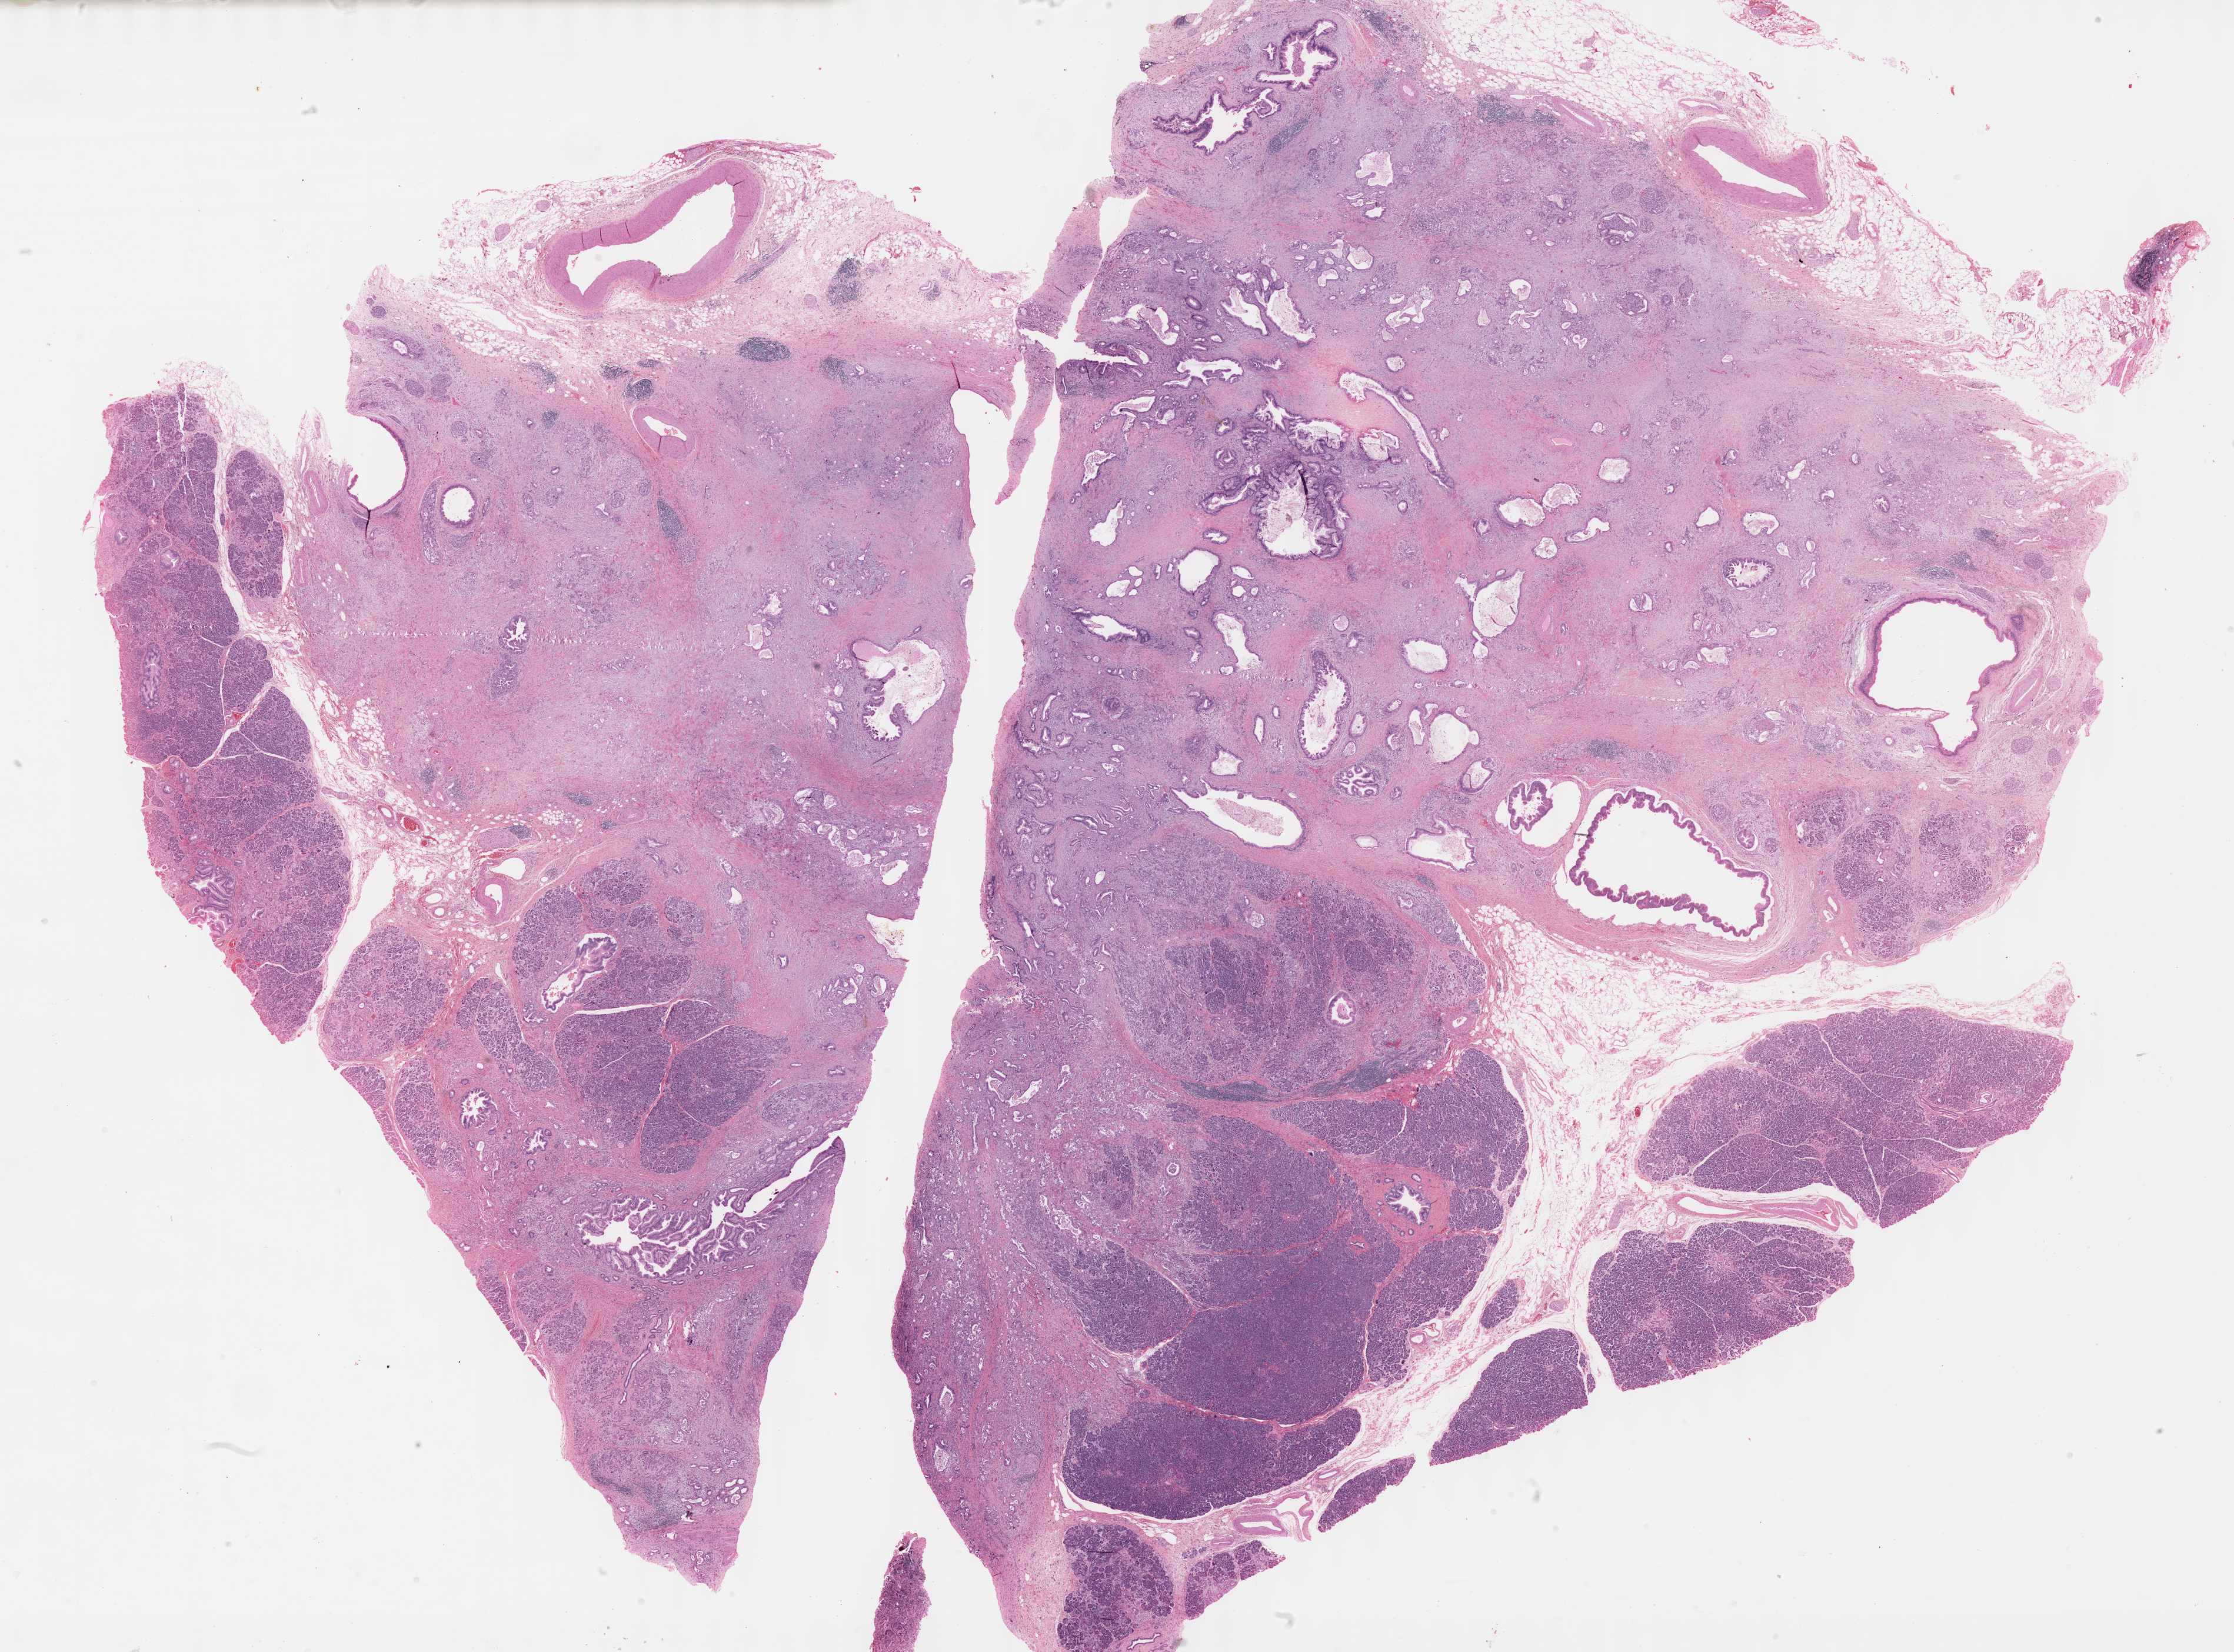
Whole-slide histology image, H&E, shown as a low-resolution overview of the whole scanned area (about 30.7 x 22.7 mm, acquisition: 40x scan), formalin-fixed paraffin-embedded (FFPE) diagnostic section, sample: primary tumour, pancreas. Patient: female, age at initial diagnosis 53 years.
Pathologic diagnosis: Infiltrating duct carcinoma, NOS (head of pancreas).